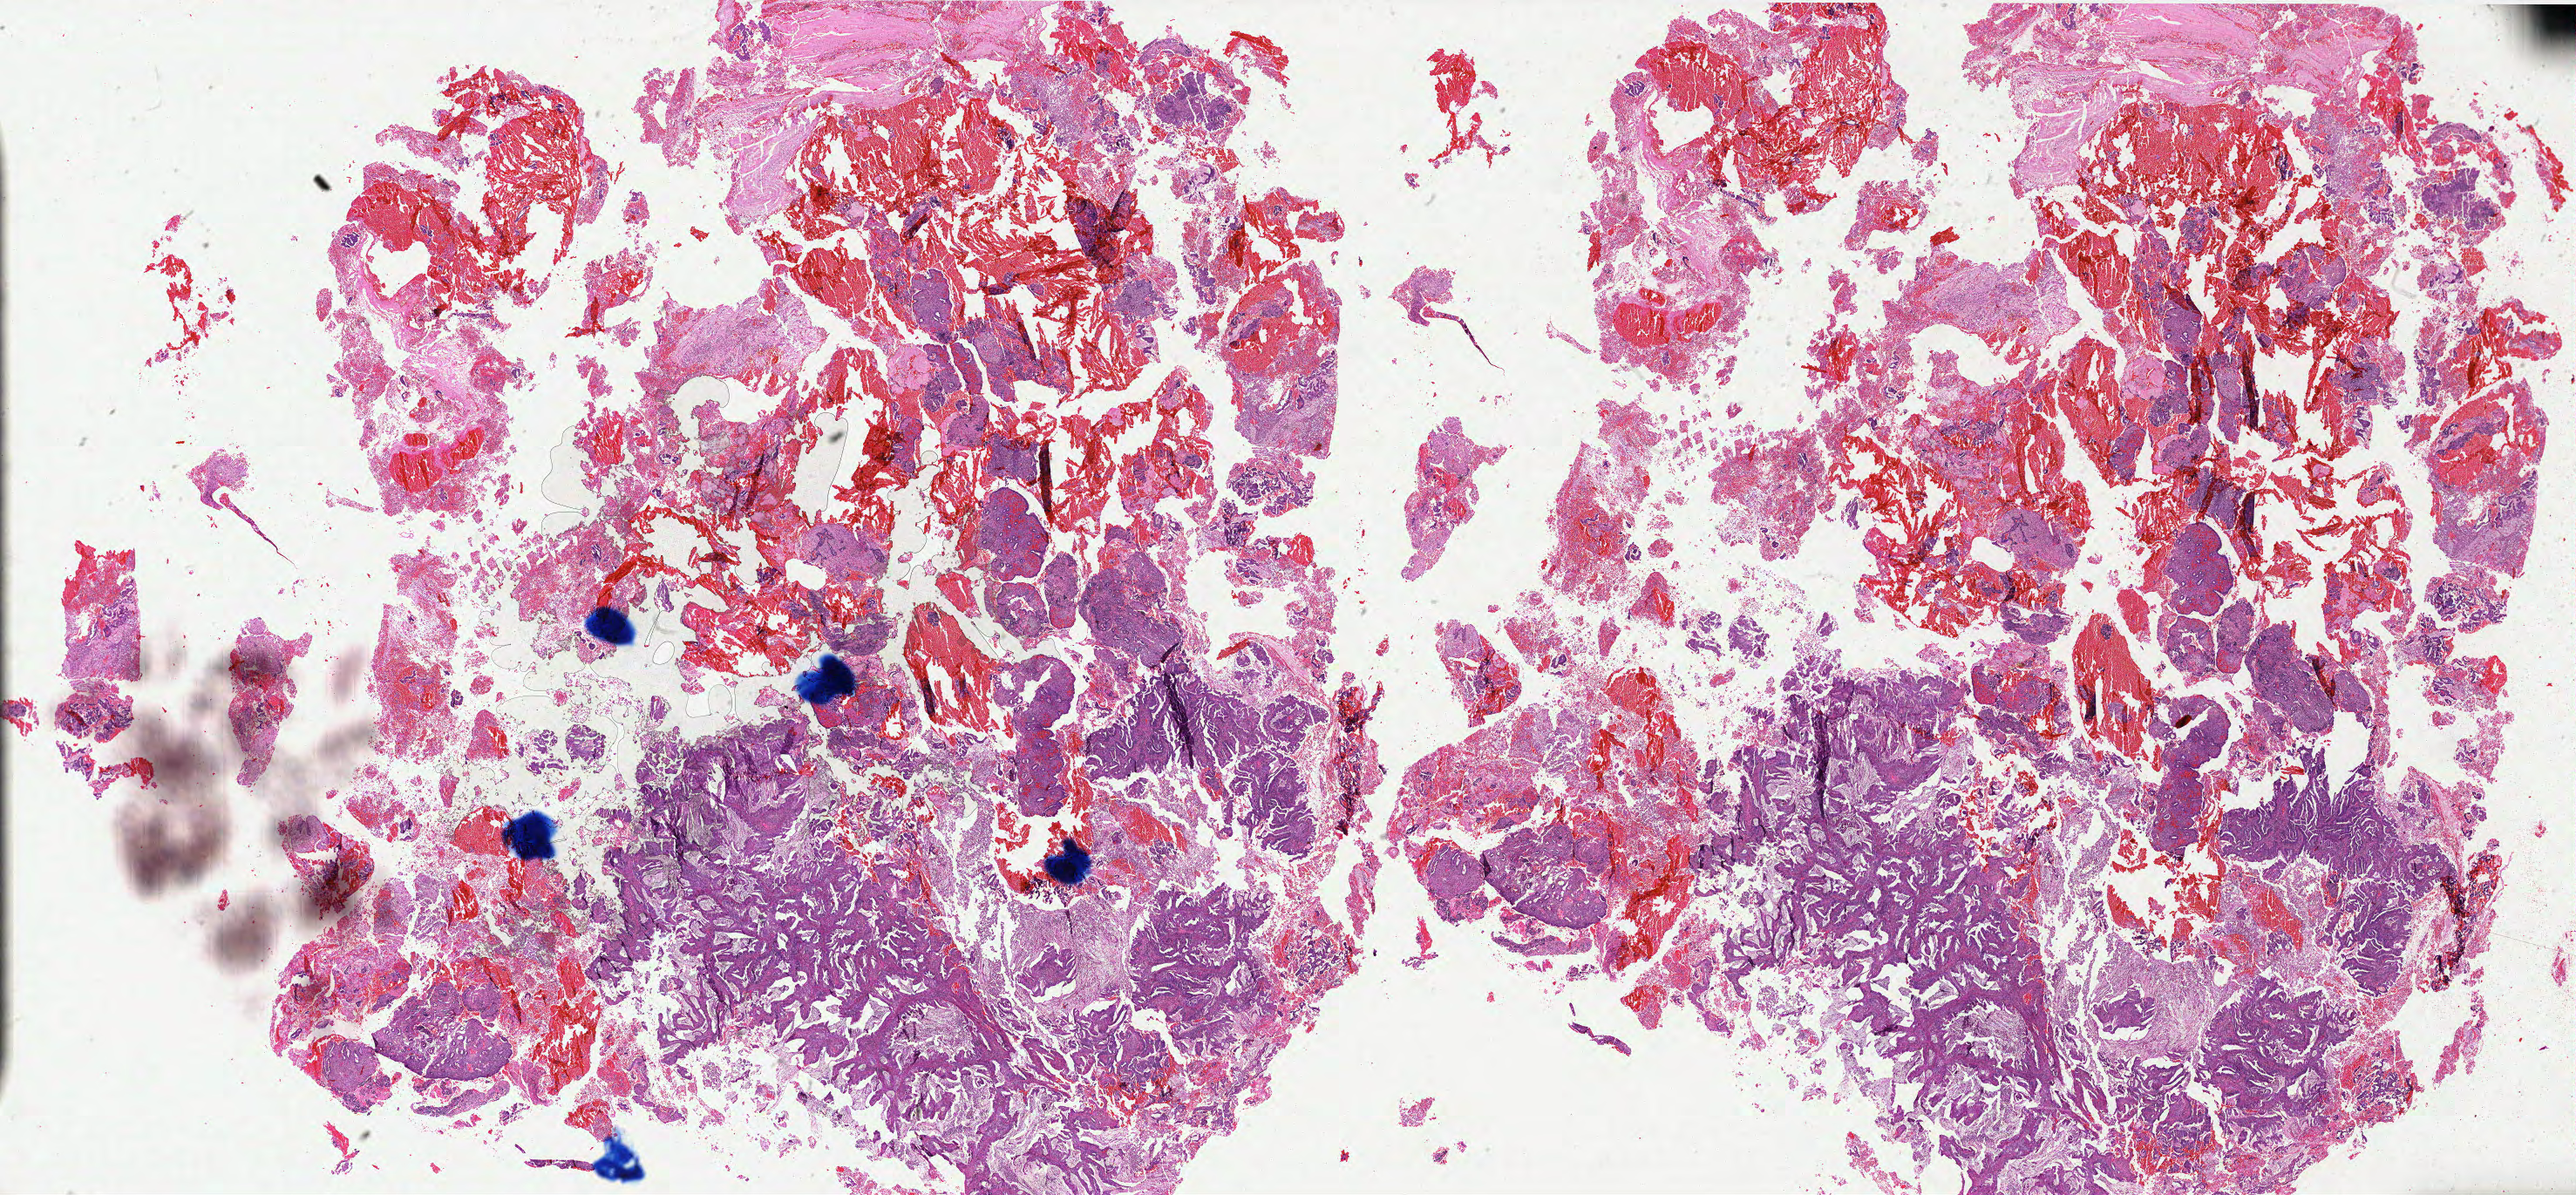
Digitized H&E-stained tissue section (whole slide), low-resolution overview of the scanned area, about 47.3 x 21.9 mm (acquisition: 40x scan). Formalin-fixed paraffin-embedded (FFPE) diagnostic section. Cervix, primary tumour sample. Female patient; age at initial diagnosis 24 years. Histologic grade: G2 (moderately differentiated).
FIGO stage: IB2. Diagnosis: Mucinous adenocarcinoma, endocervical type (cervix uteri).